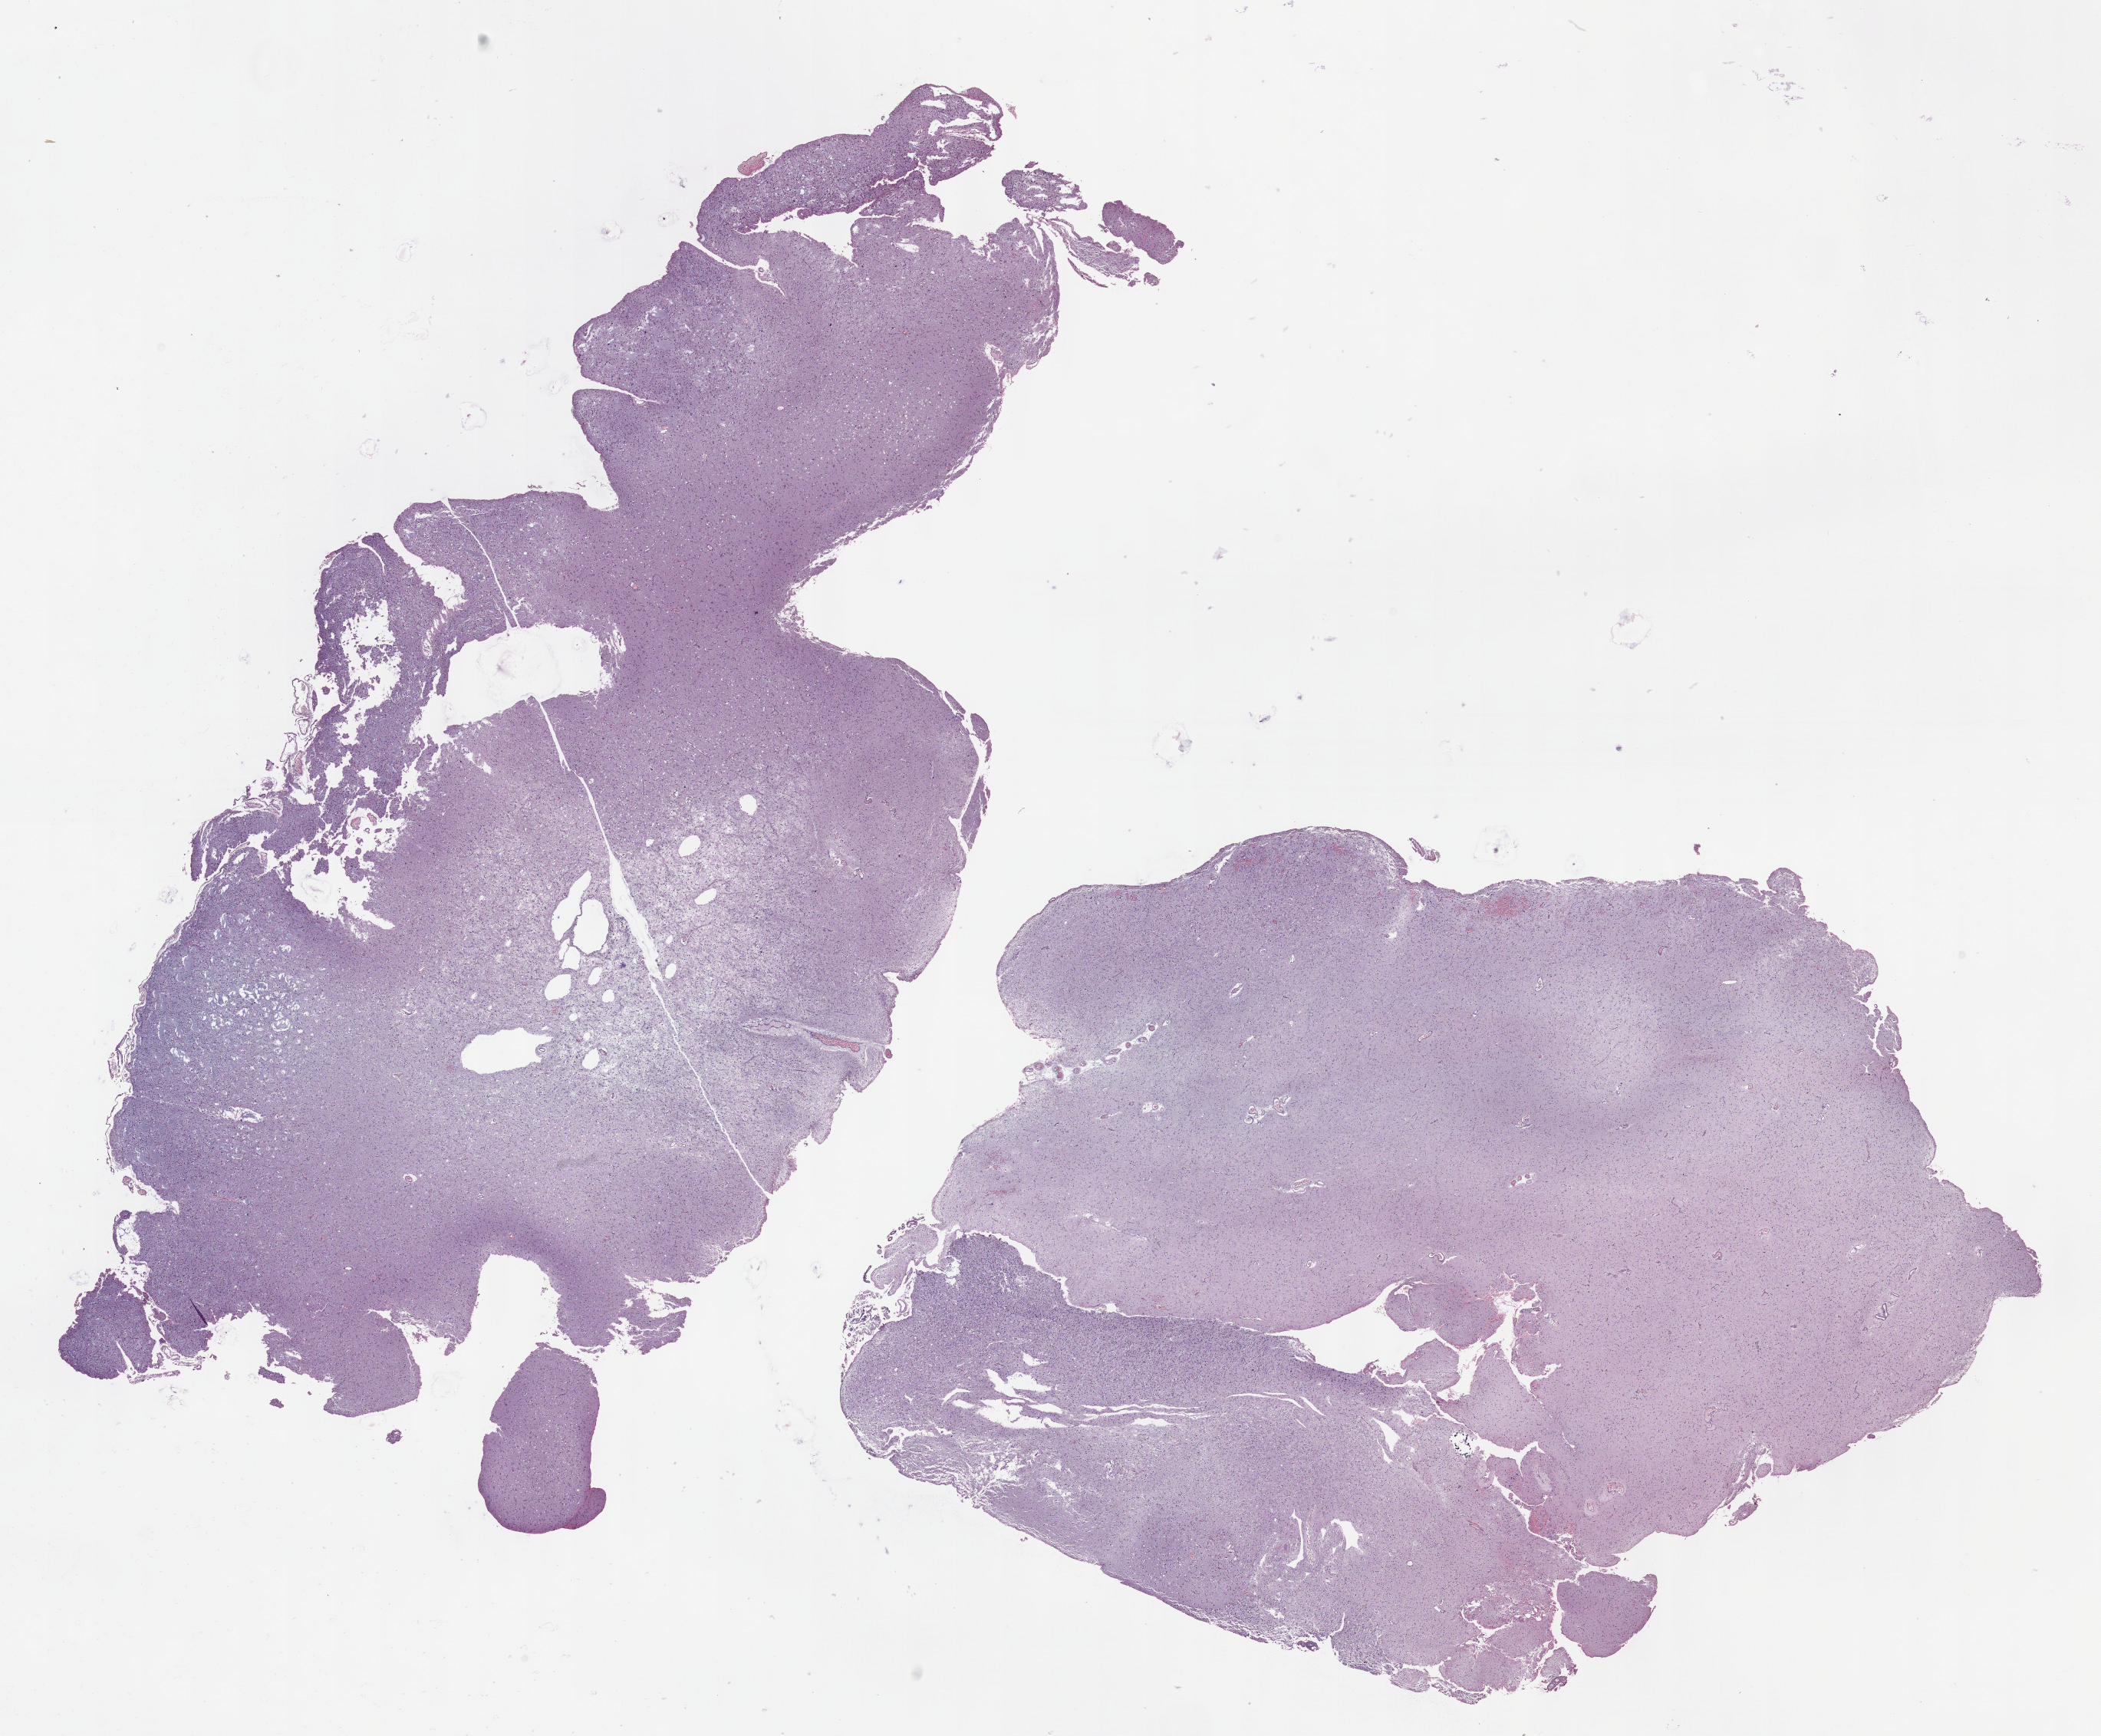
Digitized H&E-stained tissue section (whole slide) — whole scanned area (about 22.1 x 18.3 mm, slide scanned at 40x) shown as a low-resolution overview. FFPE section. Sample: primary tumour, brain. Patient: female, age at initial diagnosis 52 years. Histologic grade: G2 (moderately differentiated).
Diagnosis: Astrocytoma, NOS (cerebrum).